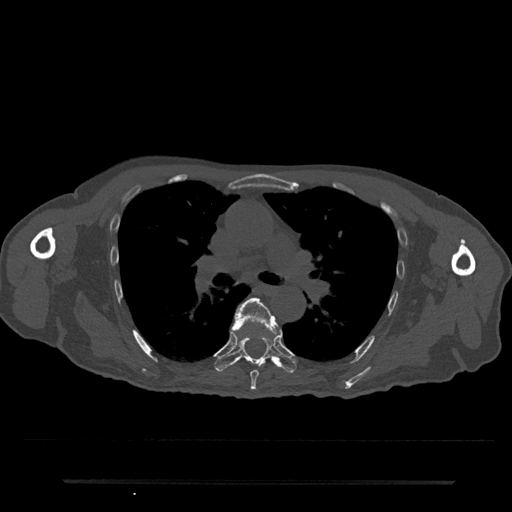
CT including the spine, one axial slice; position 503 of 797 along the scan axis; bone window (W 1800 / L 400 HU); 0.5 mm slice thickness; 512 × 512 image matrix, field of view 427 × 427 mm. Patient: male, 74 years. Case-level facts recorded for this patient, not image findings: primary cancer: prostate.
Outlined on this slice (semi-automatic segmentation, software-assisted and operator-edited):
- T6 vertebra: bounding box (x1, y1, x2, y2) in pixels: (231, 298, 279, 391)
- T7 vertebra: (214, 336, 297, 372)